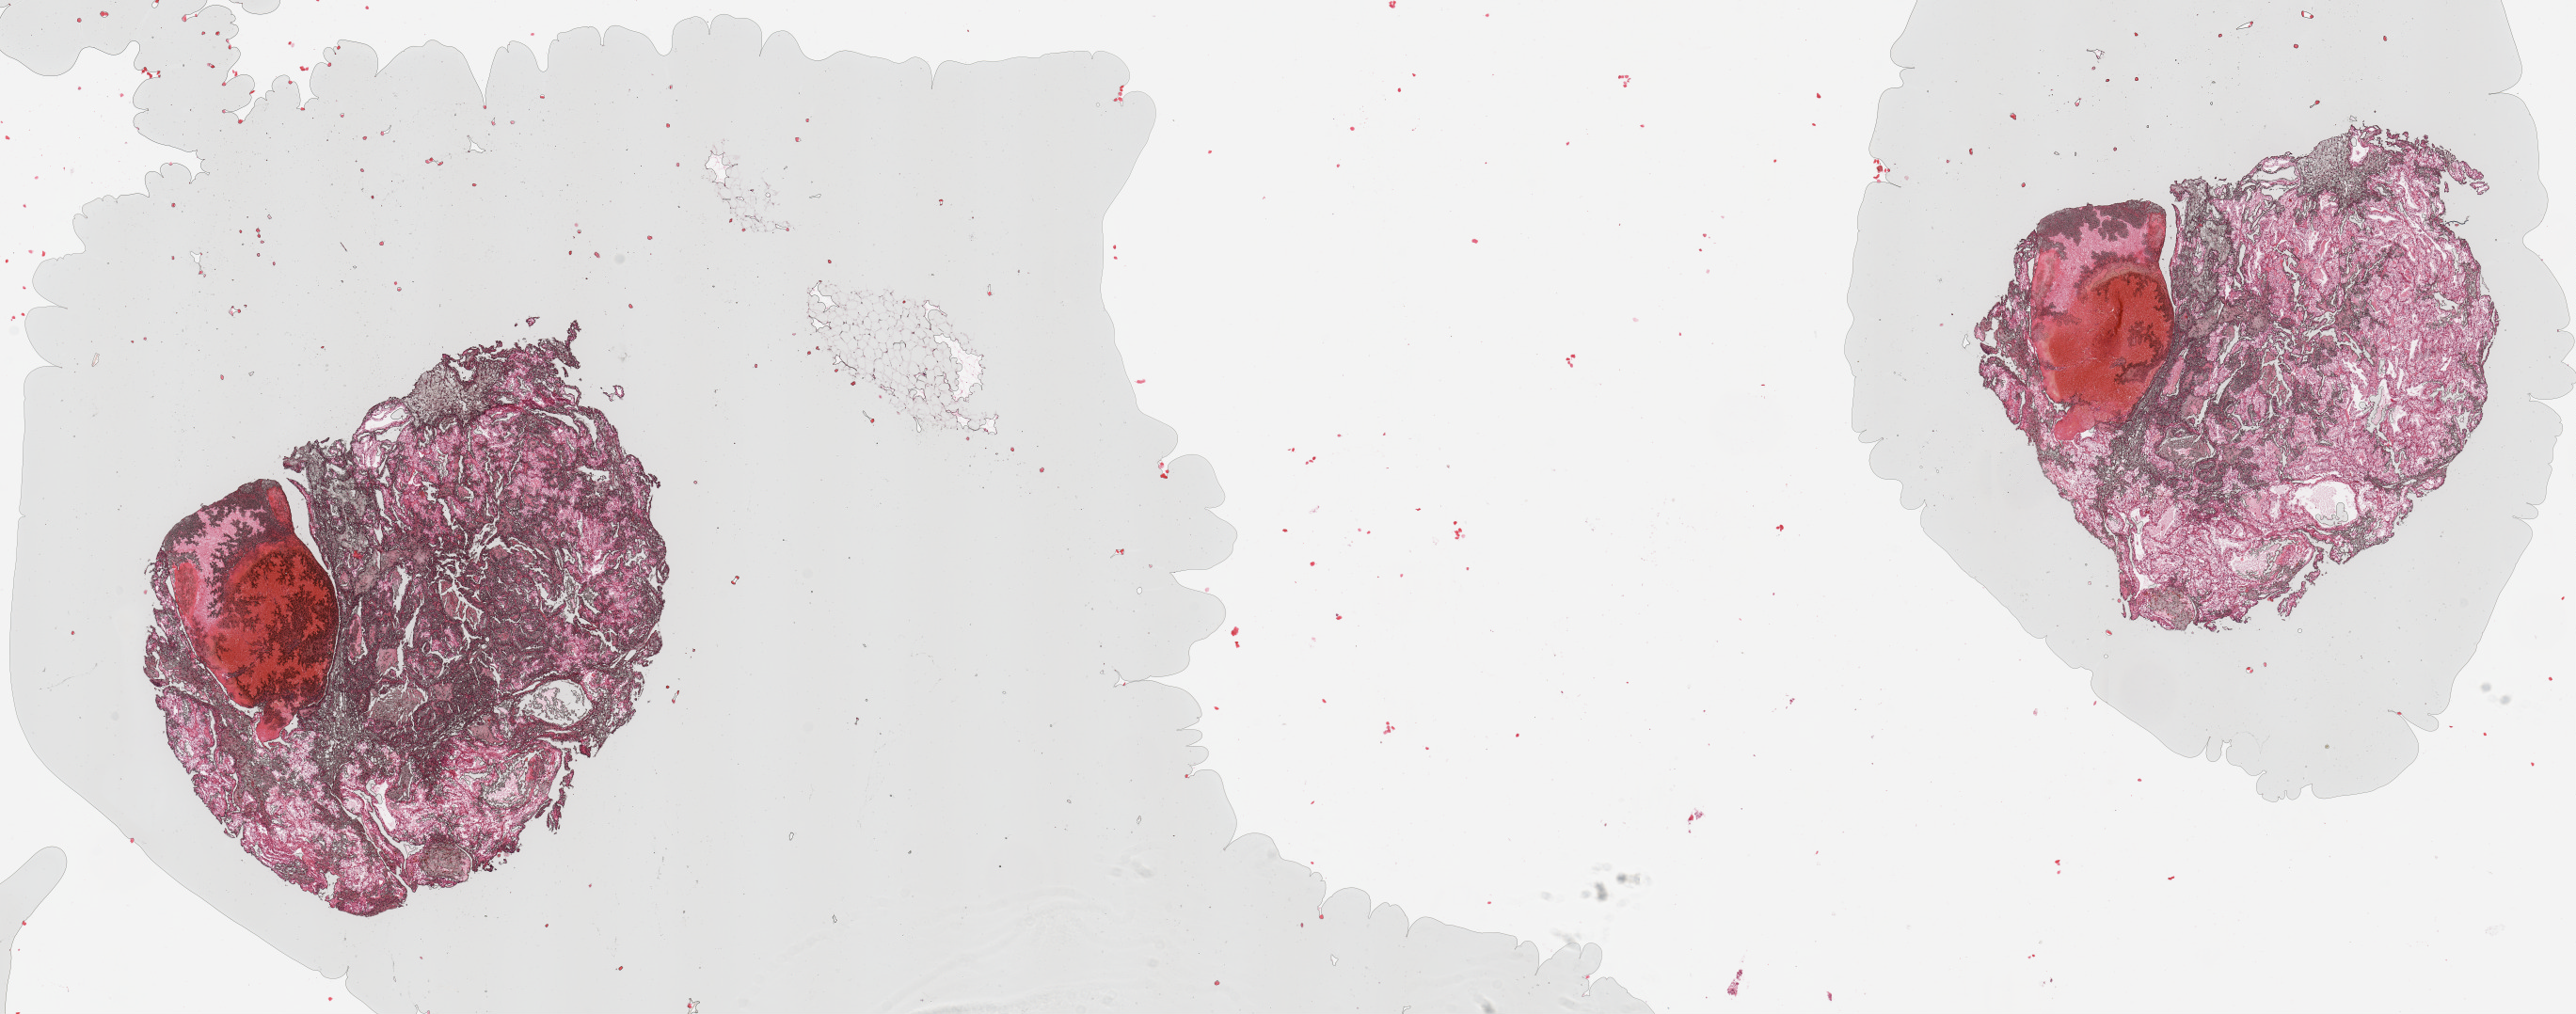
Whole-slide histology image, H&E — low-resolution overview of the scanned area, about 21.7 x 8.5 mm, tumour tissue sample, kidney. 52-year-old male patient. Histologic grade: G2 (moderately differentiated).
- AJCC pathologic stage: II
- primary tumour site (as recorded): upper pole
- histologic diagnosis: Renal cell carcinoma, NOS